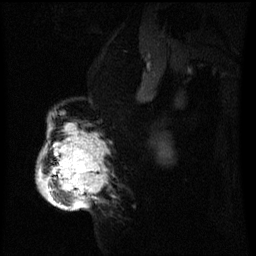
Breast MRI (dynamic contrast-enhanced), one sagittal slice; position 40 of 60 along the scan axis; dynamic contrast-enhanced series, image 2 of 3 at this slice position (ordered by acquisition); 1.5 T; TE 4.2 ms, TR 8 ms; 2.2 mm slice thickness; 256 × 256 image matrix. Patient: female, 50 years.
Annotated regions visible in this slice (semi-automatically segmented with operator editing):
- analysis volume of interest (the breast-tissue region the enhancement analysis was run in; not a lesion): bounding box [x1, y1, x2, y2] px = [37, 120, 105, 209]
- tumour enhancement mask (voxels above the 70 % enhancement threshold inside the analysis volume of interest): [38, 126, 105, 209]